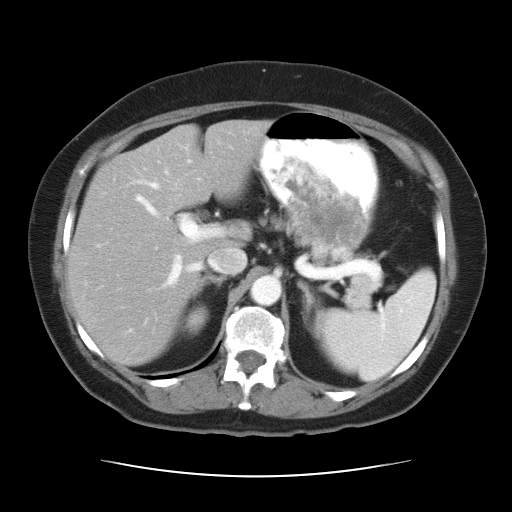
Contrast-enhanced abdominal CT, one axial slice. Slice 20 of 34 in the series (ordered by position). Soft-tissue window (W 400 / L 40 HU). 7.5 mm slice thickness. 512 × 512 image matrix, field of view 360 × 360 mm. Female patient, age 65 years. Case-level facts recorded for this patient, not image findings: diagnosis: colorectal cancer liver metastases, imaged before liver resection; multiple liver metastases: yes; largest metastasis: 2.2 cm; disease in both lobes: no.
Structures marked on this image (expert manual segmentation):
- hepatic veins: bounding box [x1, y1, x2, y2] px = [132, 169, 245, 273]
- liver: [66, 122, 262, 364]
- planned liver remnant (the part of the liver to remain after resection): [66, 122, 262, 364]
- portal vein (with intrahepatic branches): [135, 194, 221, 325]